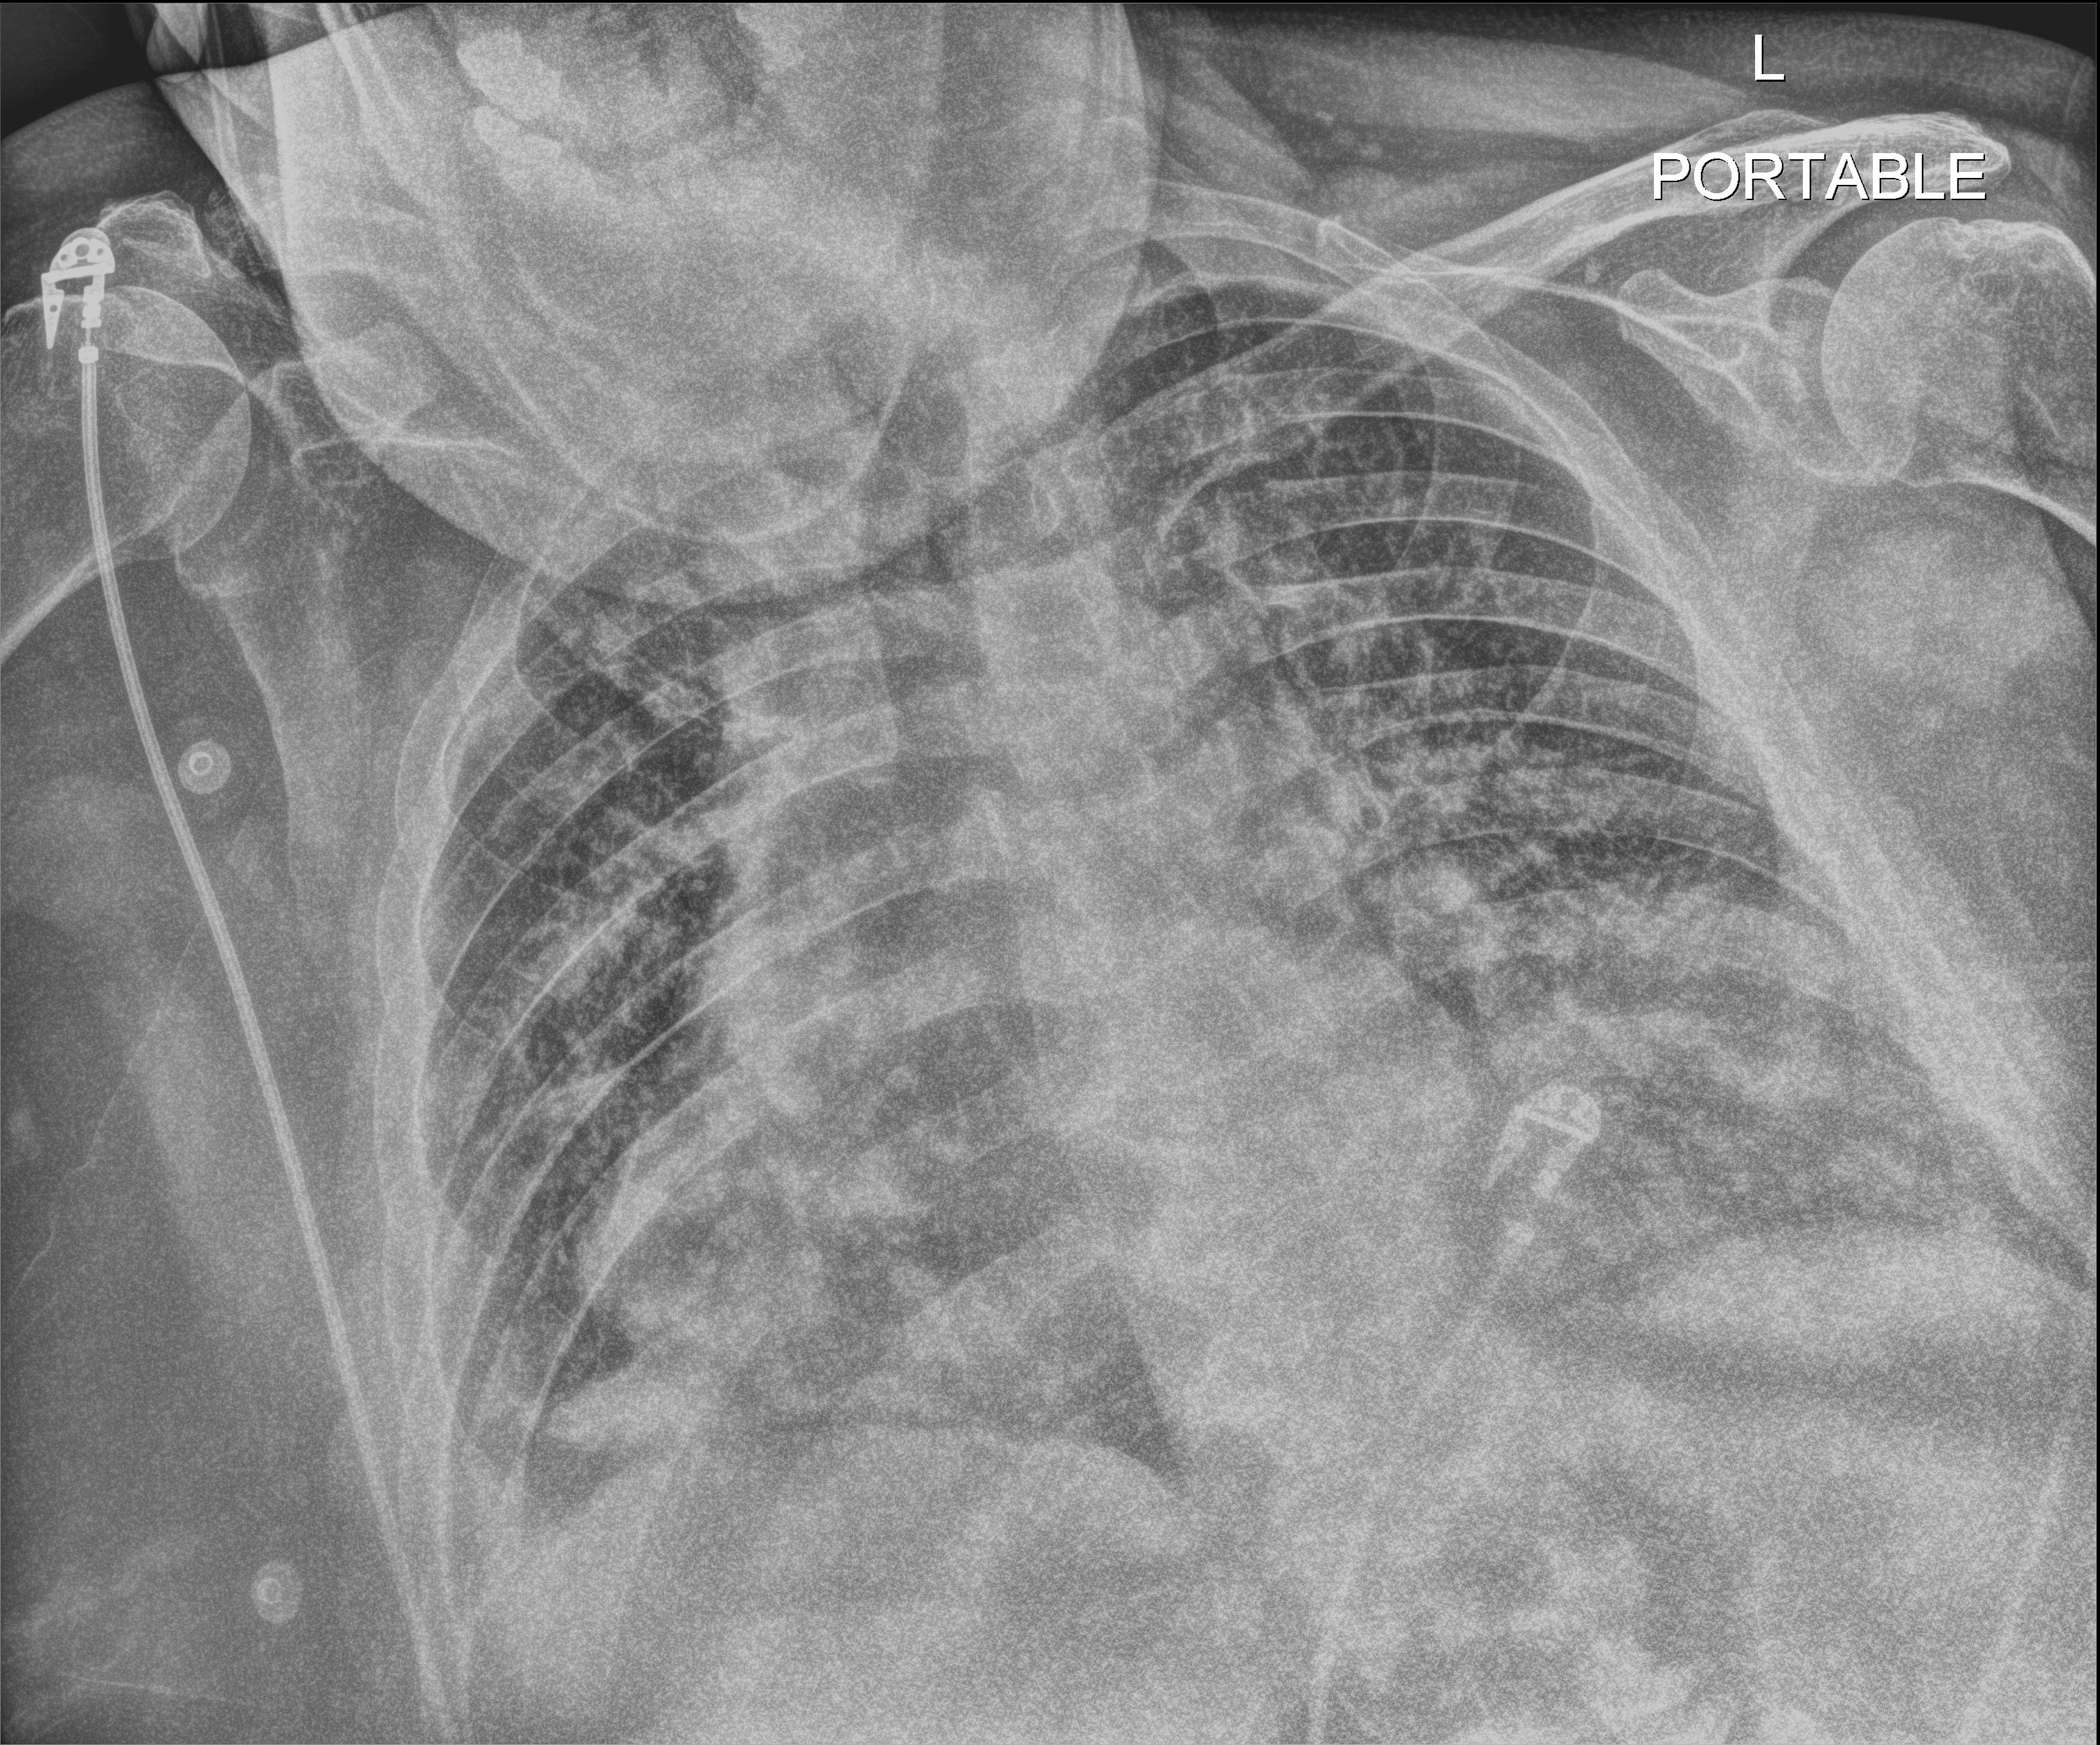
Chest X-ray, anteroposterior (AP) projection. Patient hospitalised with COVID-19; male, aged 60–74 years.
Hospital-stay facts (about this admission, not read from this image; timing relative to this image not recorded): mechanically ventilated during this hospital stay: yes.